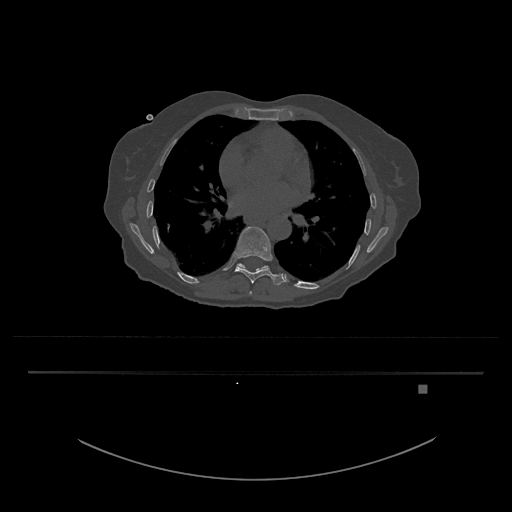
CT including the spine, one axial slice; position 753 of 797 along the scan axis; reconstruction kernel Br40s/3; 120 kVp; bone window (W 1800 / L 400 HU); 0.5 mm slice thickness; 512 × 512 image matrix, field of view 500 × 500 mm. Patient: female, 57 years. From the clinical record (not read from this slice): primary cancer: cervical.
Annotated regions visible in this slice (semi-automatic segmentation, software-assisted and operator-edited):
- T10 vertebra: bounding box <236,263,269,272> (left, top, right, bottom; pixels)
- T8 vertebra: <249,291,252,295>
- T9 vertebra: <235,226,284,285>